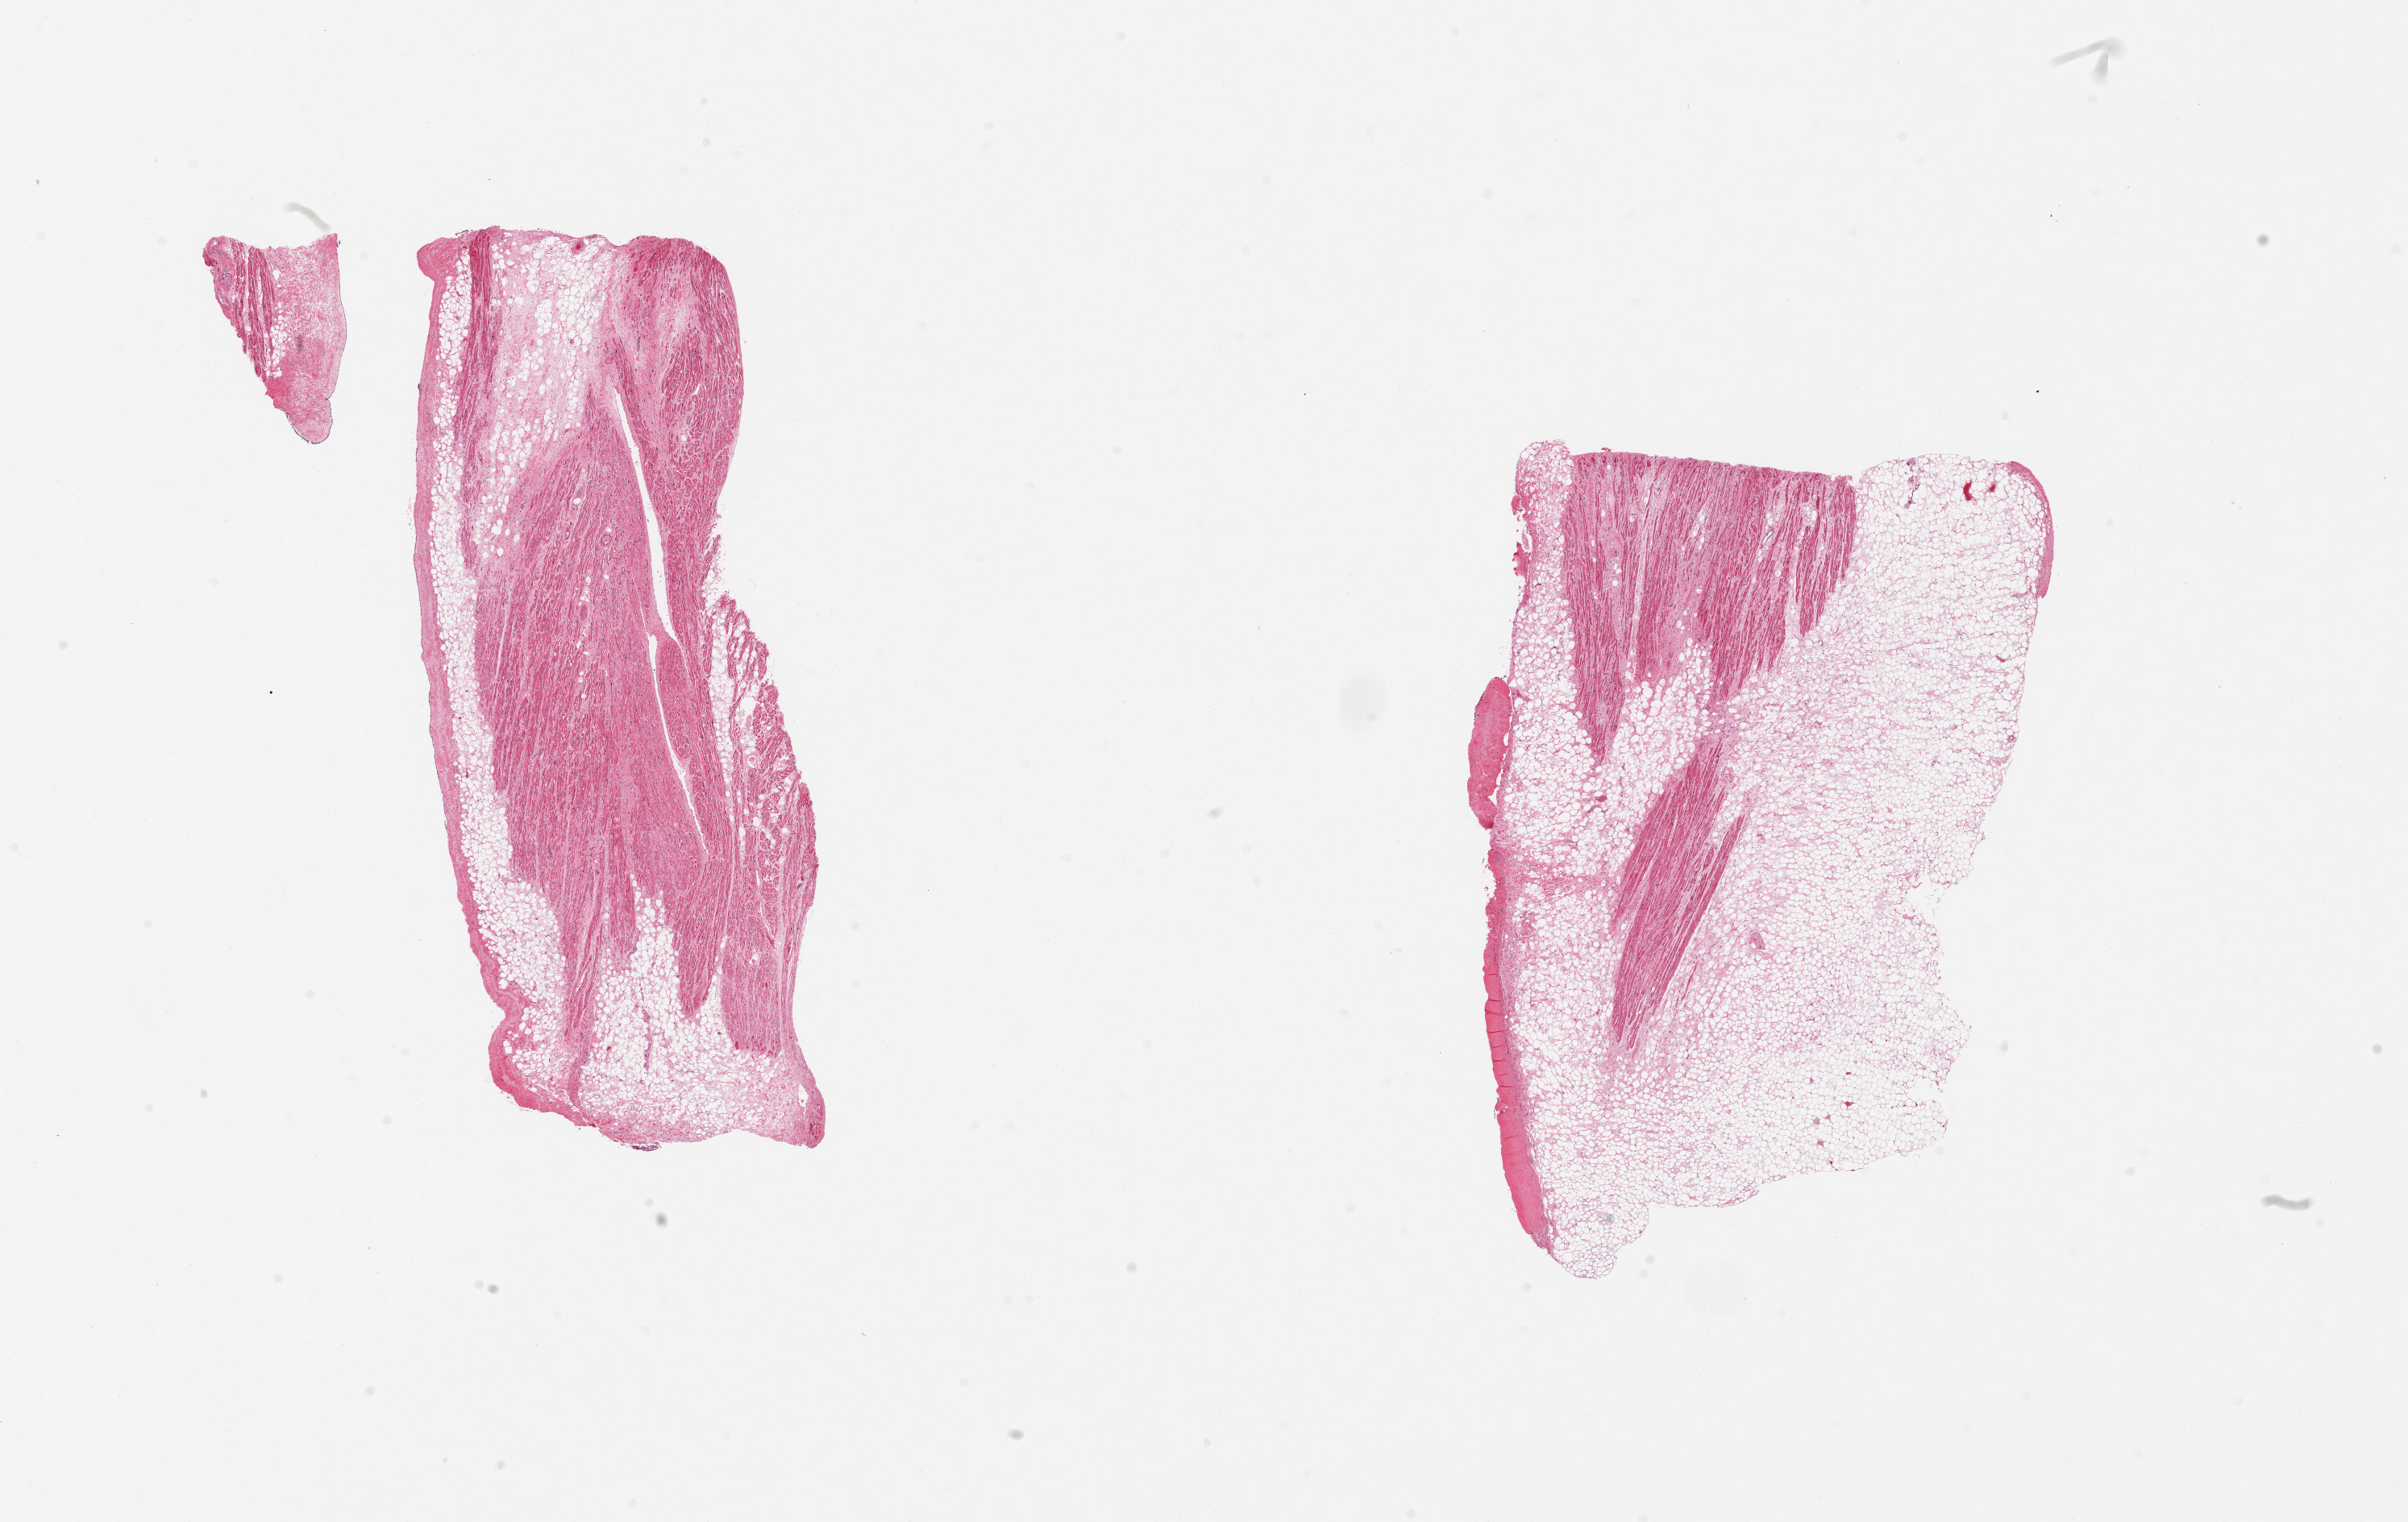
Digitized hematoxylin and eosin (H&E)-stained section — shown as a low-resolution overview of the whole scanned area (about 23.6 x 14.9 mm, from a 20x scan); PAXgene-fixed, paraffin-embedded tissue; sampled site (target tissue): auricular appendage; tissue donor sample. Male donor.
- review note (as recorded): 2 pieces, no abnormalities; ~50% adipose tissue